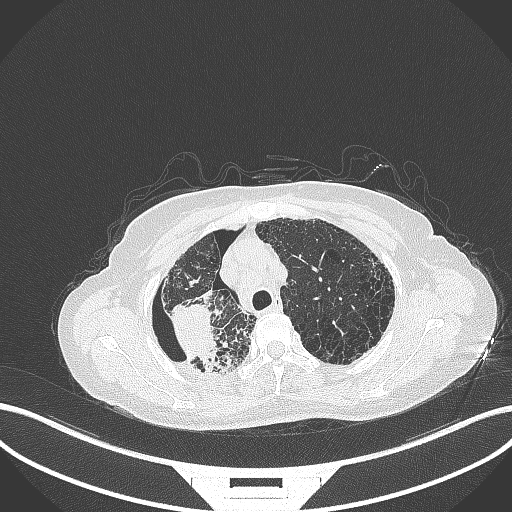
Chest CT, one axial slice; slice 278 of 408 in the series (ordered by position); 120 kVp; lung window (W 1500 / L -600 HU); 512 × 512 image matrix, field of view 400 × 400 mm. Patient: female, 64 years. From the clinical record (not read from this slice): clinical TNM (as recorded): T3 N3 M0.
Annotated regions visible in this slice (rectangle marked by the reading radiologist):
- lung tumour (recorded histology: squamous cell carcinoma): bounding box [x1, y1, x2, y2] px = [167, 299, 224, 367]